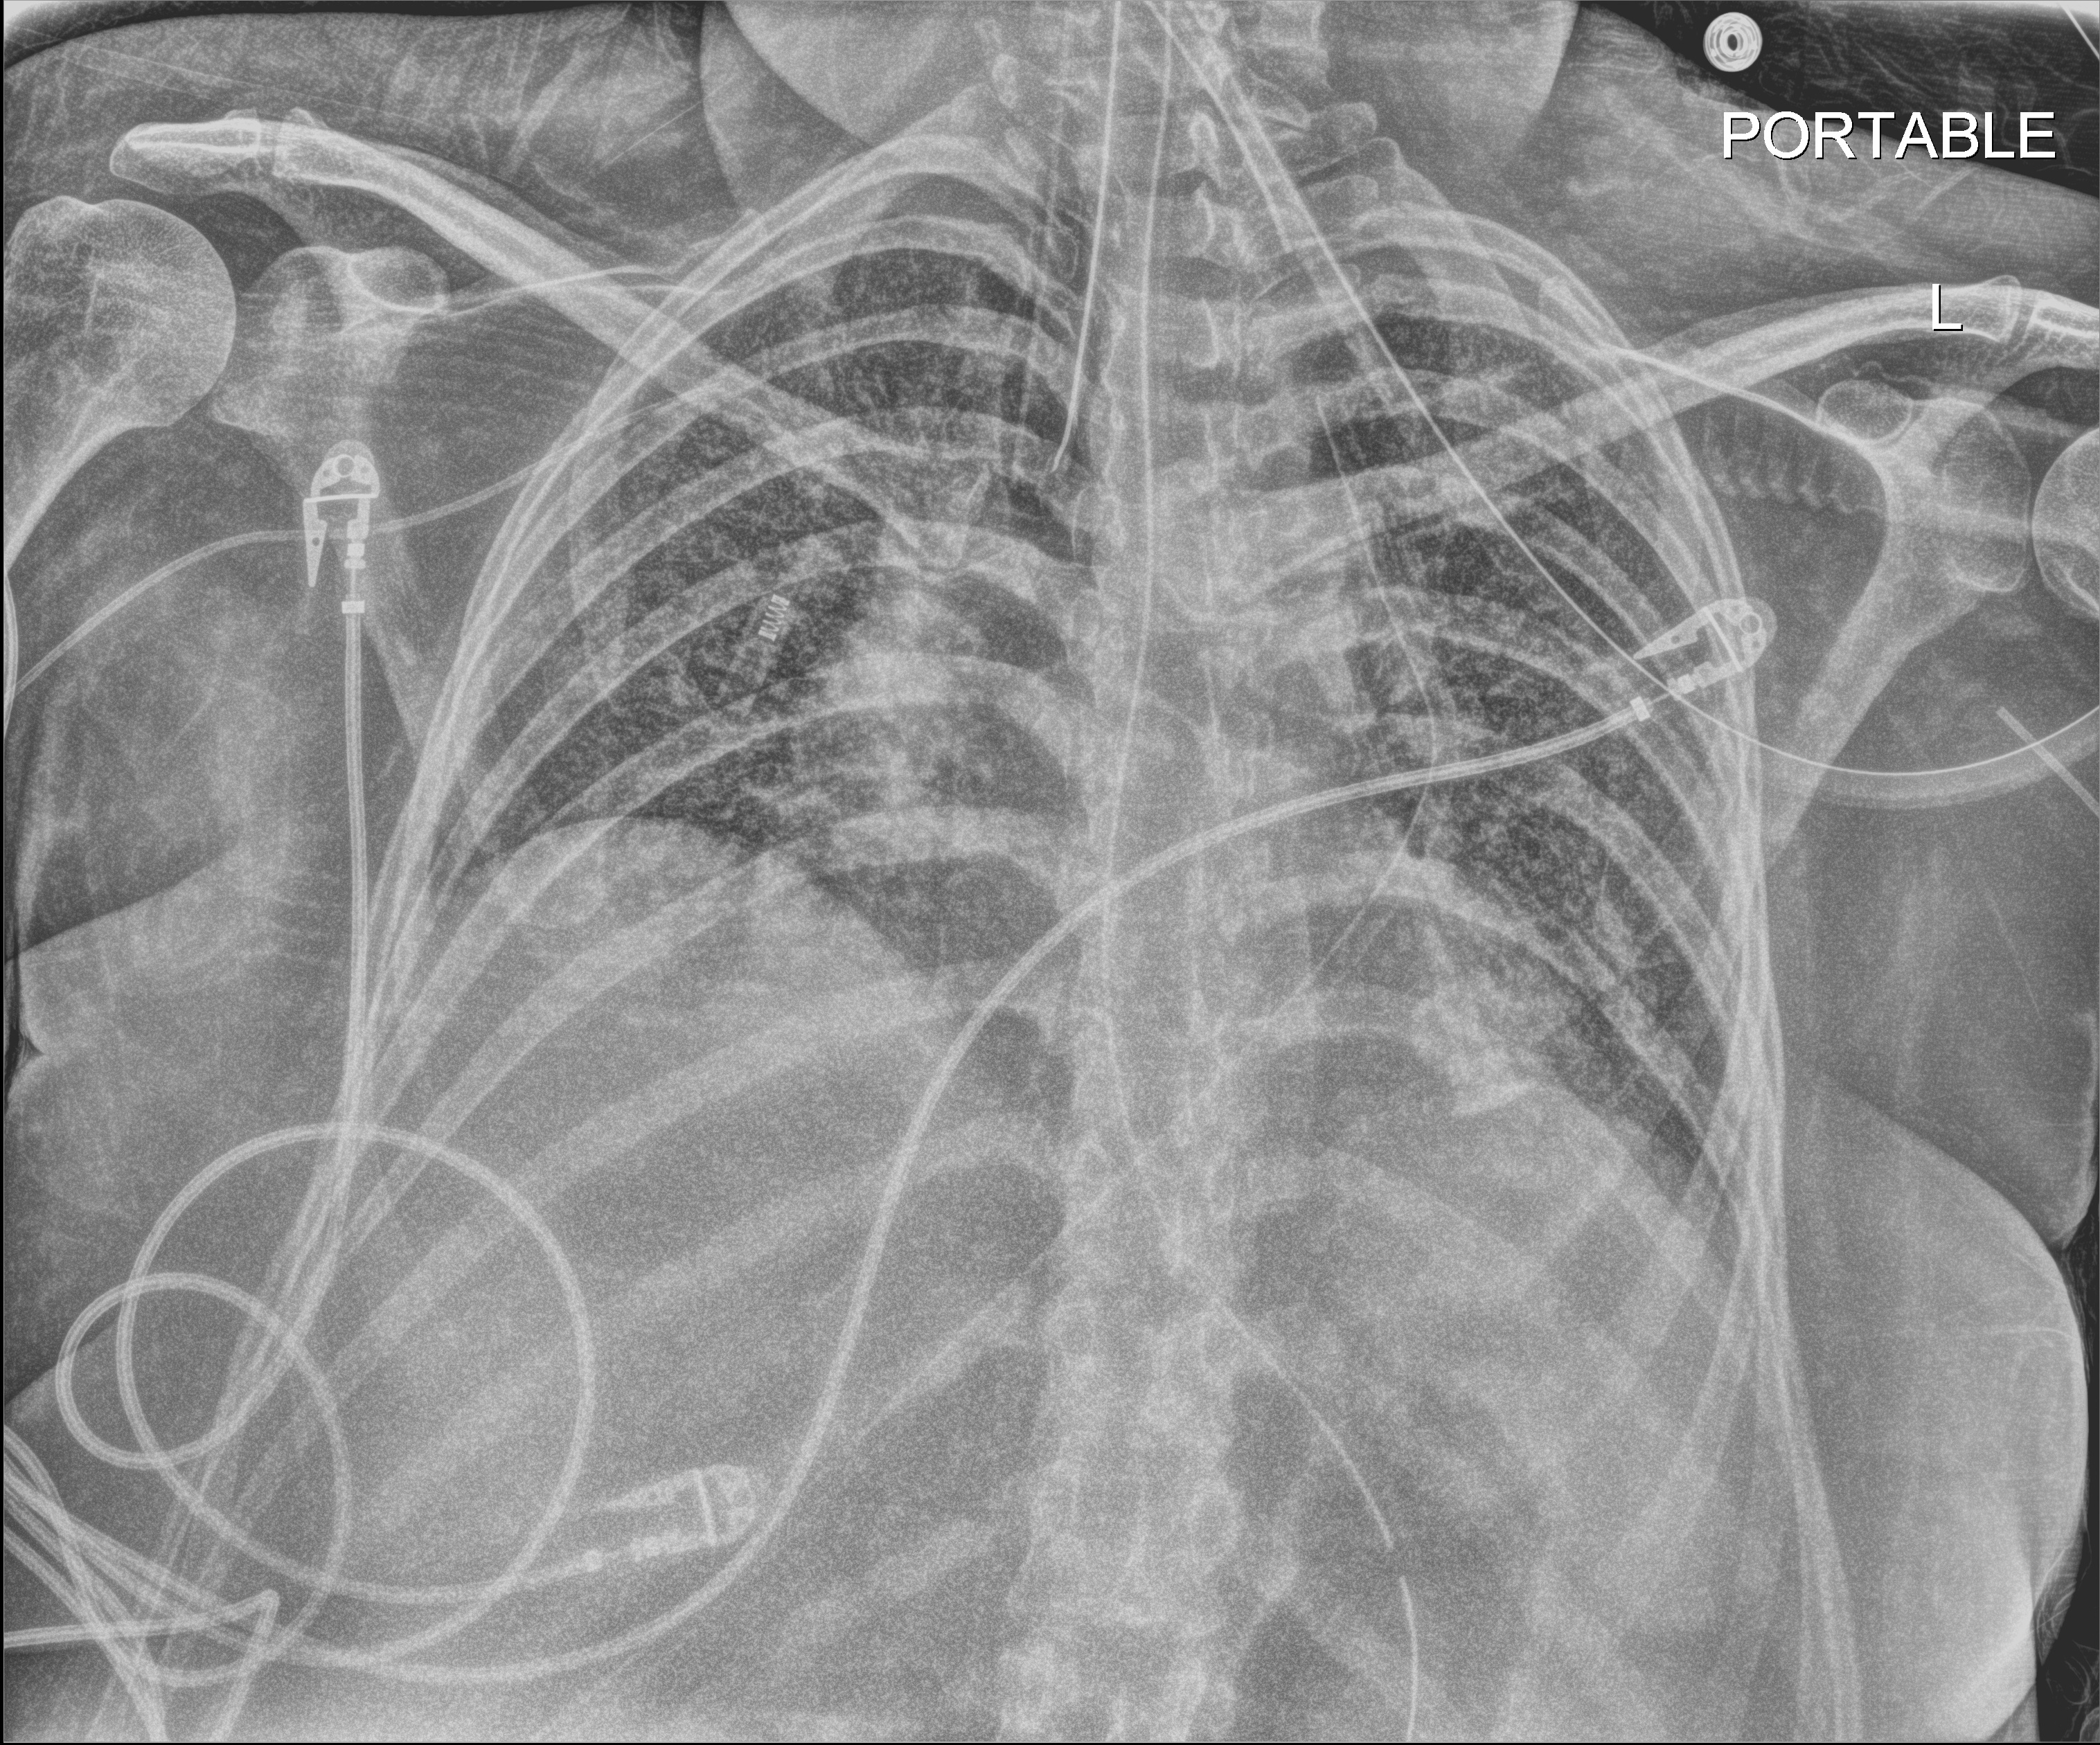
Portable chest radiograph; anteroposterior (AP) projection. Female patient hospitalised with COVID-19, age 18–59 years.
Admission-level facts for this patient (not findings on this image; timing relative to this image not recorded): other chronic lung disease (admission record): yes; diabetes (admission record): no; smoking status (admission record): former.